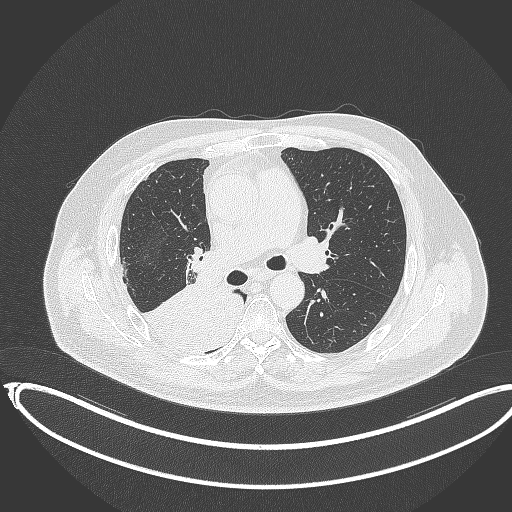
Chest CT, one axial slice; position 212 of 403 along the scan axis; reconstruction kernel B70f; 120 kVp; lung window (W 1500 / L -600 HU); 1 mm slice thickness; 512 × 512 image matrix, field of view 436 × 436 mm. Patient: male, 68 years. From the clinical record (not read from this slice): clinical TNM (as recorded): T2a N0 M0.
Outlined on this slice (bounding box drawn by a radiologist):
- lung tumour (recorded histology: adenocarcinoma): box from (x=146, y=288) to (x=251, y=356) px